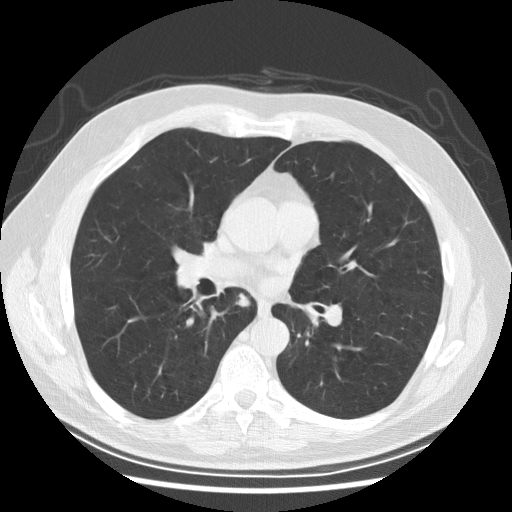
Low-dose screening chest CT, axial slice. Second annual screen. Lung window (W 1500 / L -600 HU). 2.5 mm slice thickness. Male, age 61 years at enrolment.
- Expert-annotated lung lesion, box from (x=224, y=284) to (x=256, y=318) px.
- Screening reader's record for this exam: no non-calcified nodule ≥4 mm recorded.
- Official screen result: negative screen, minor abnormalities not suspicious for lung cancer.
- Lung cancer was diagnosed 382 days after this screen: squamous cell carcinoma, keratinizing, NOS, right lower lobe, stage IIIB (AJCC 6th edition), 40 mm at pathology.